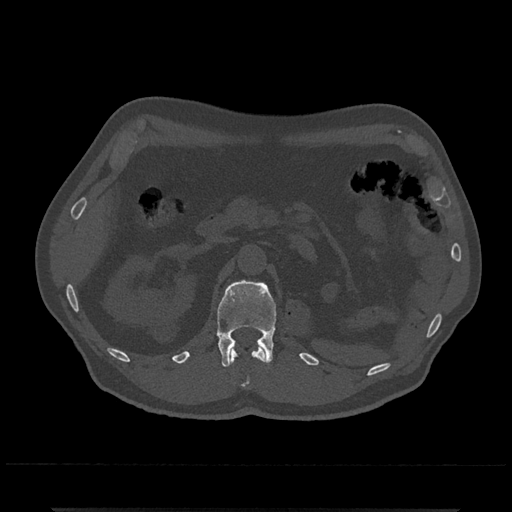
CT including the spine, one axial slice; position 380 of 797 along the scan axis; 120 kVp; bone window (W 1800 / L 400 HU); 0.5 mm slice thickness; 512 × 512 image matrix. Male patient, age 67 years. From the clinical record (not read from this slice): primary cancer: prostate.
Structures marked on this image (semi-automatically segmented with operator editing):
- L1 vertebra: bounding box <216,280,276,367> (left, top, right, bottom; pixels)
- T12 vertebra: <229,346,266,388>